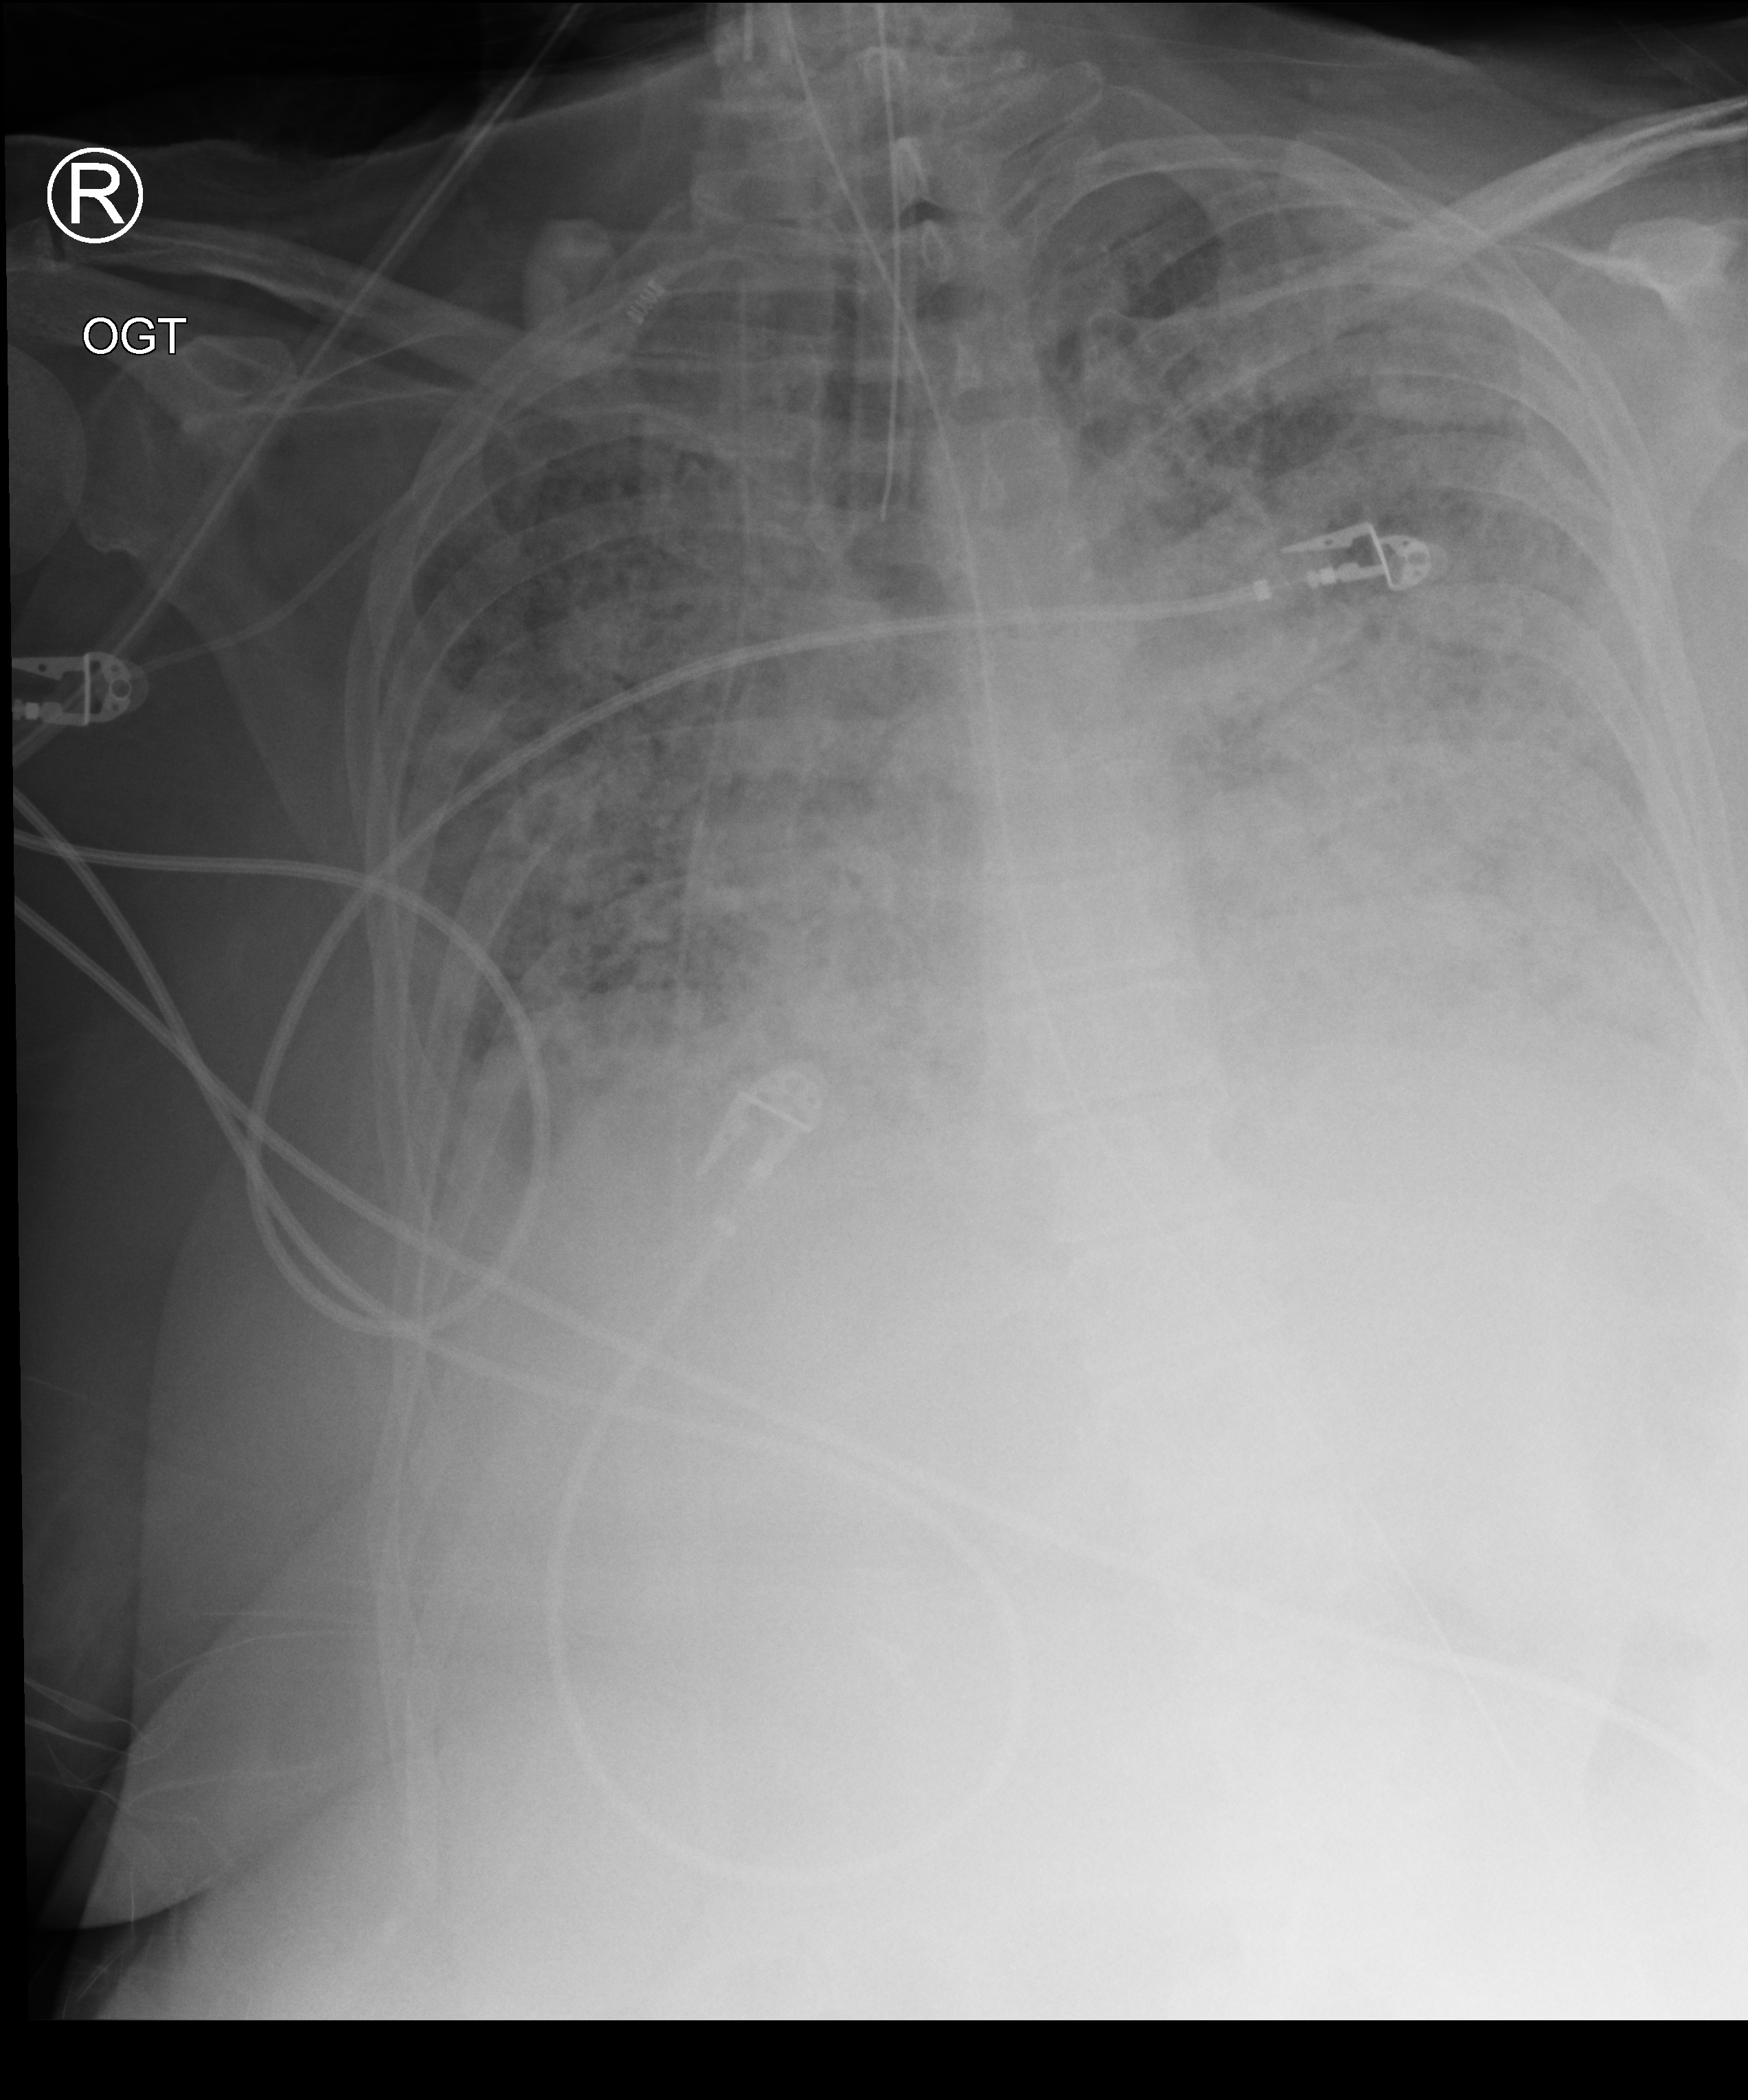
Bedside chest radiograph (computed radiography); anteroposterior (AP) projection. Patient hospitalised with COVID-19; female, aged 60–74 years.
From the hospital-stay record, not from the radiograph (when in the stay this image was taken is not recorded):
- mechanically ventilated during this hospital stay: yes